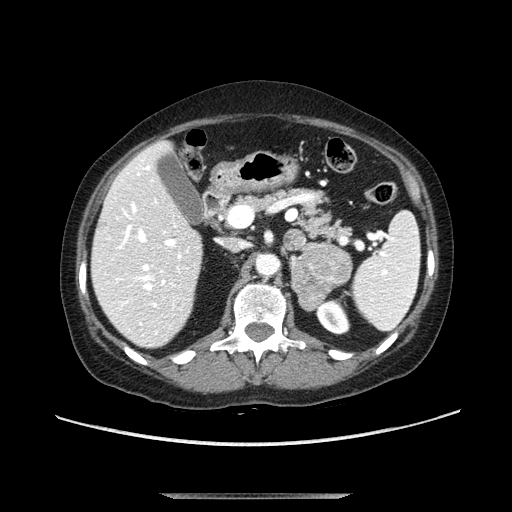
Contrast-enhanced abdominal CT, one axial slice; slice 62 of 107 in the series (ordered by position); soft-tissue window (W 400 / L 40 HU); 2.5 mm slice thickness; 512 × 512 image matrix, field of view 380 × 380 mm. Female patient. From the clinical record (not read from this slice): diagnosis: adrenocortical carcinoma; tumour side: left adrenal; tumour size at pathology: 7.5 cm; Ki-67 index: 9 %; stage (as recorded): 3.
Annotated regions visible in this slice (semi-automatically segmented with operator editing):
- mass: box from (x=291, y=245) to (x=352, y=311) px